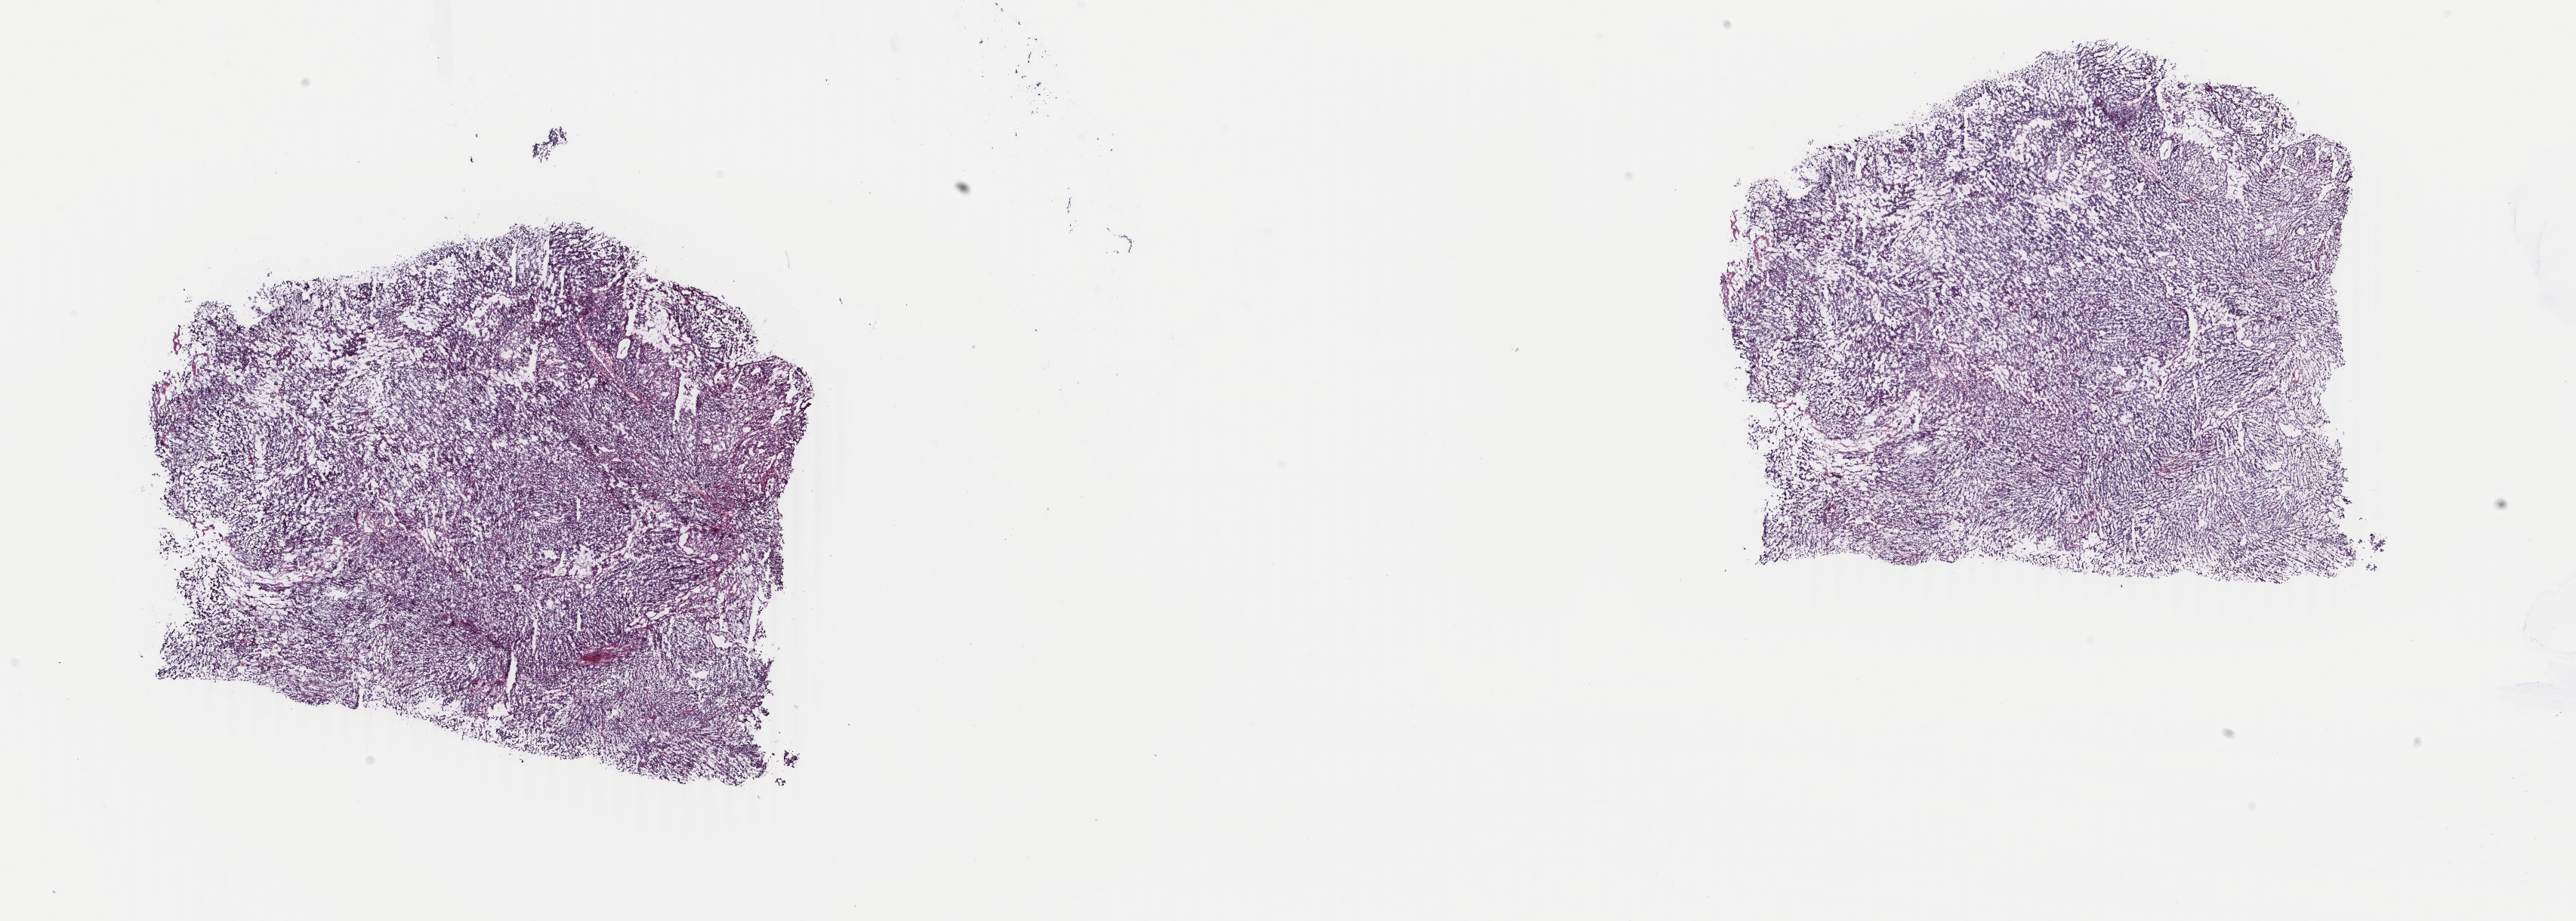
Digitized H&E-stained tissue section (whole slide) — low-resolution overview of the scanned area, about 27.1 x 9.7 mm (acquisition: 40x scan); frozen section from the top of the tissue portion; sample: primary tumour, uterus. Female, age 67 years at initial diagnosis. Pathologist review of this section (percent, as recorded): tumour cells 95%, tumour nuclei 100%, normal cells 0%, stromal cells 5%, necrosis 0%. Infiltration values recorded for this section: lymphocyte infiltration 0%, monocyte infiltration 0%, neutrophil infiltration 0%.
Diagnosis: Mullerian mixed tumor. FIGO stage: IA.